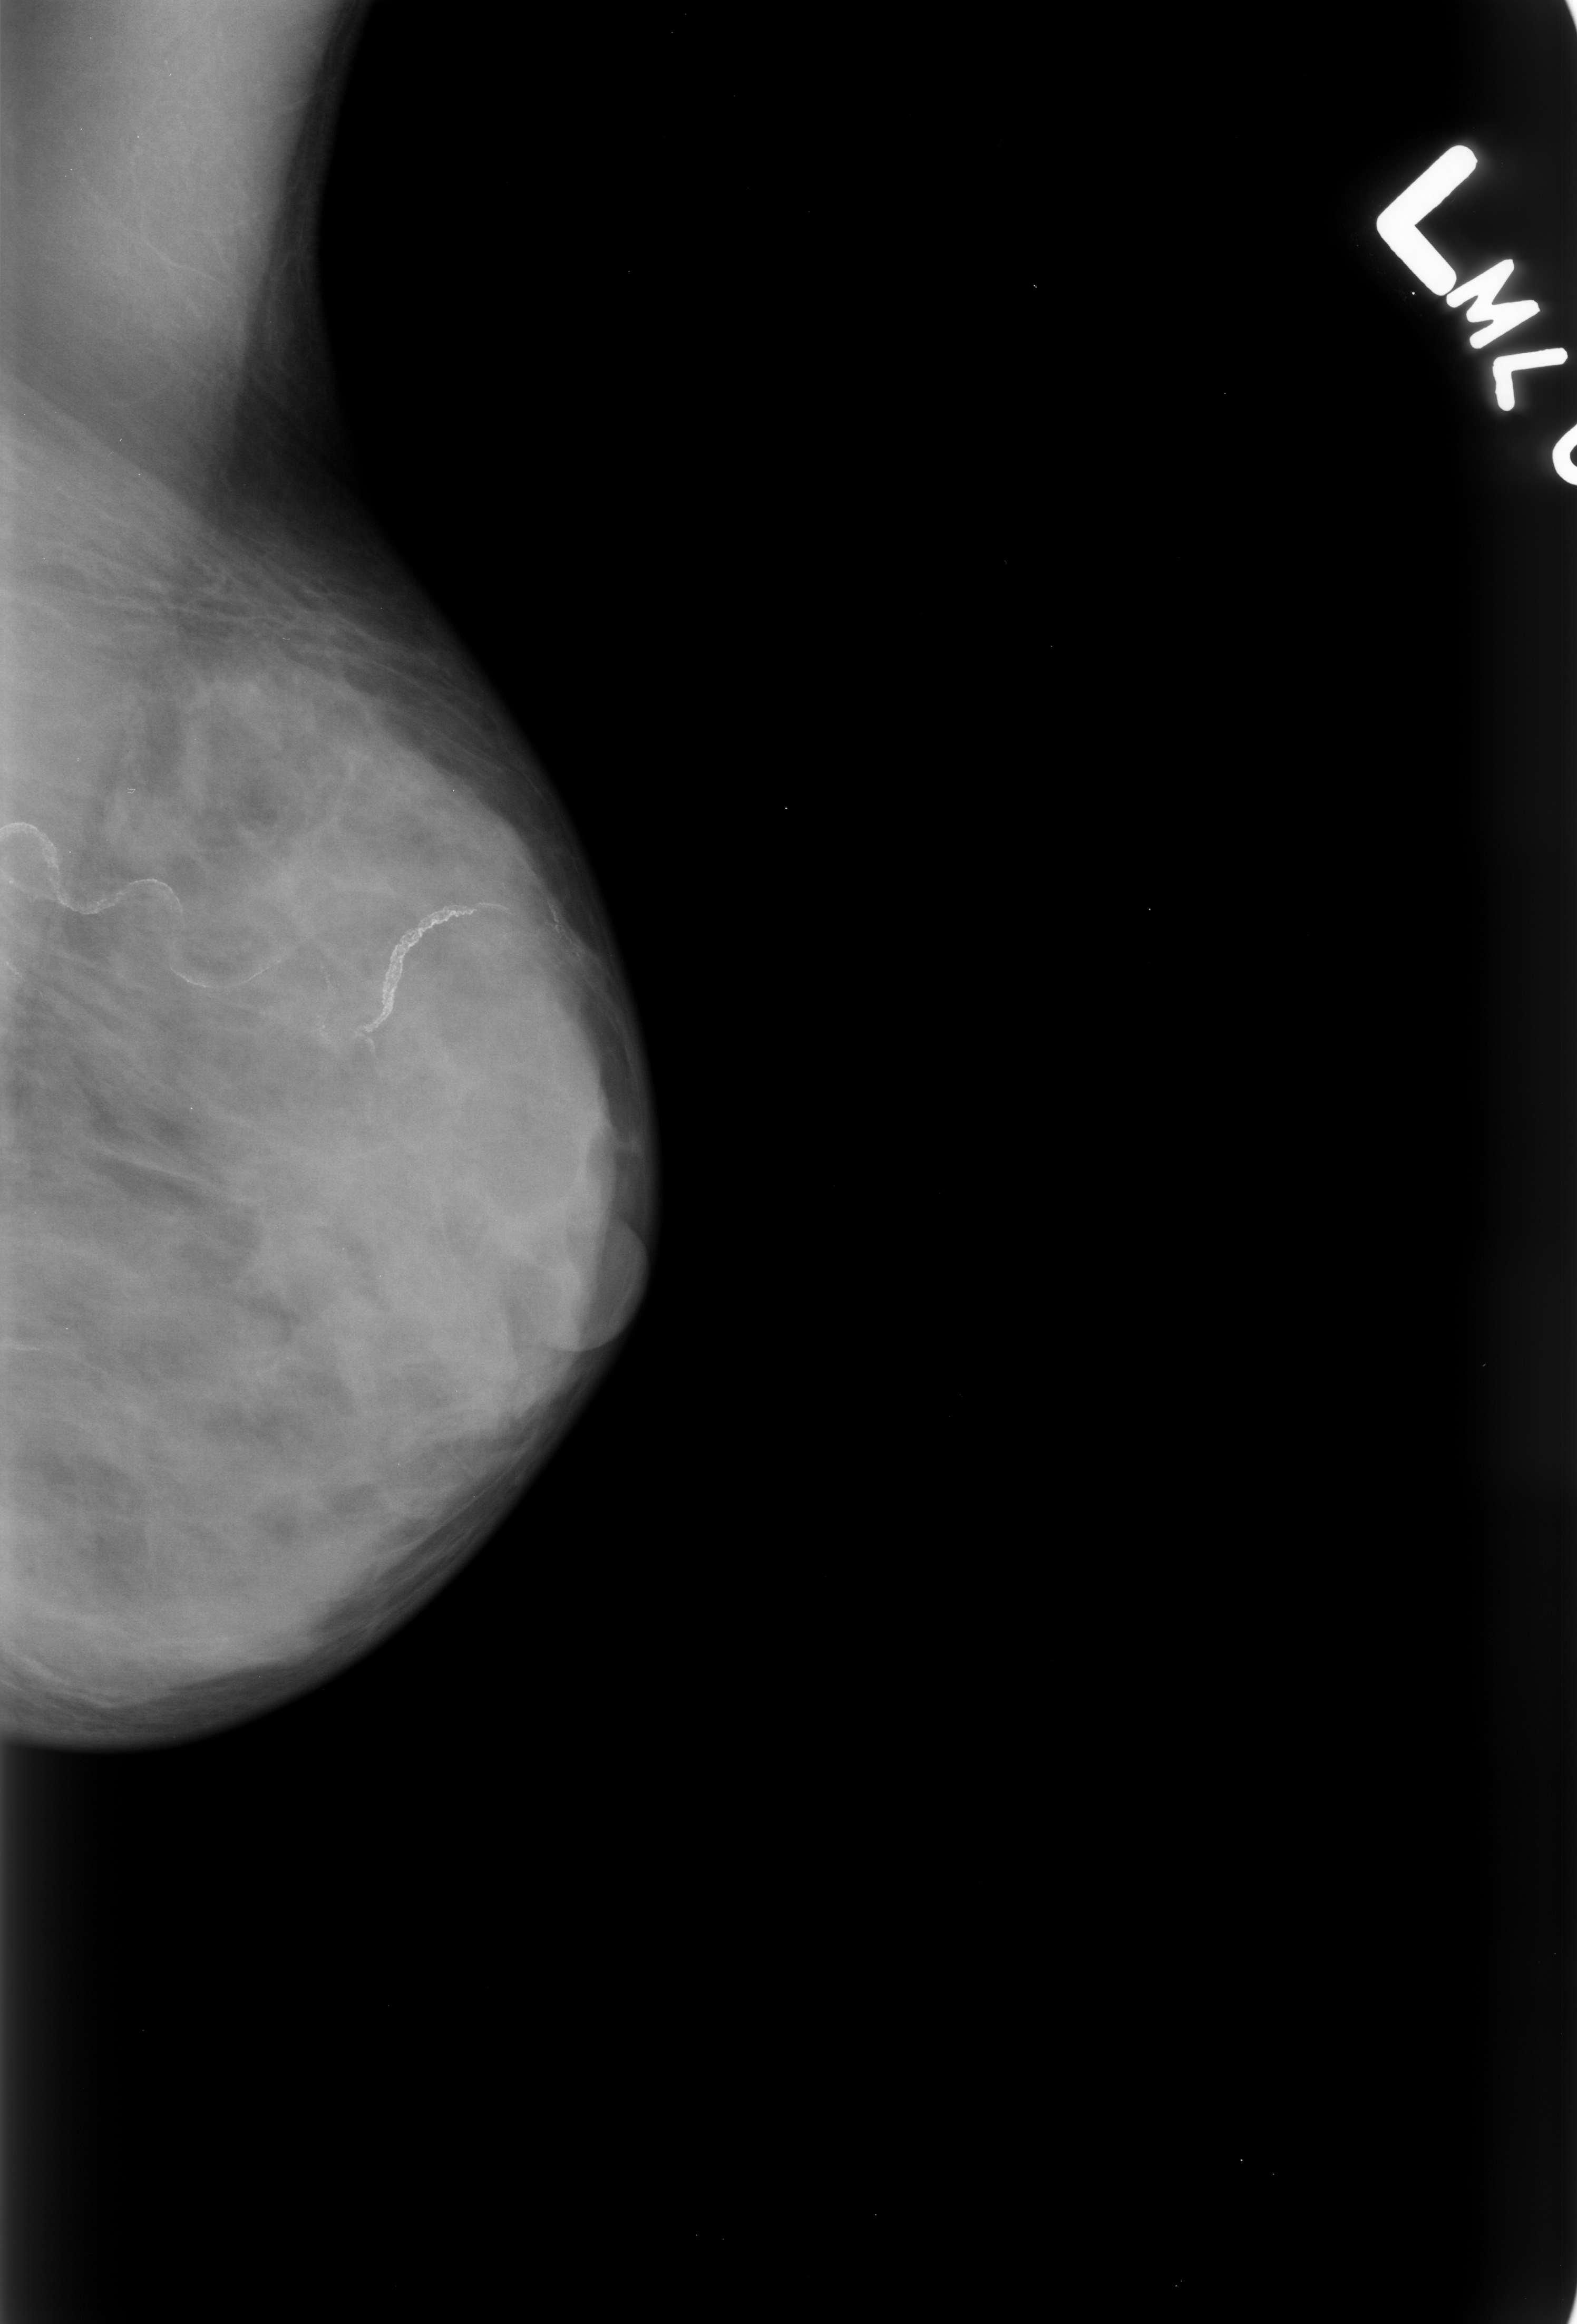
Mammogram (digitized film), left breast, mediolateral oblique (MLO) view.
Abnormality record for this image: calcifications, morphology vascular; BI-RADS assessment category 2; subtlety rating 5 on a 1 (subtle) to 5 (obvious) scale; benign; no additional work-up was recommended (benign without callback).